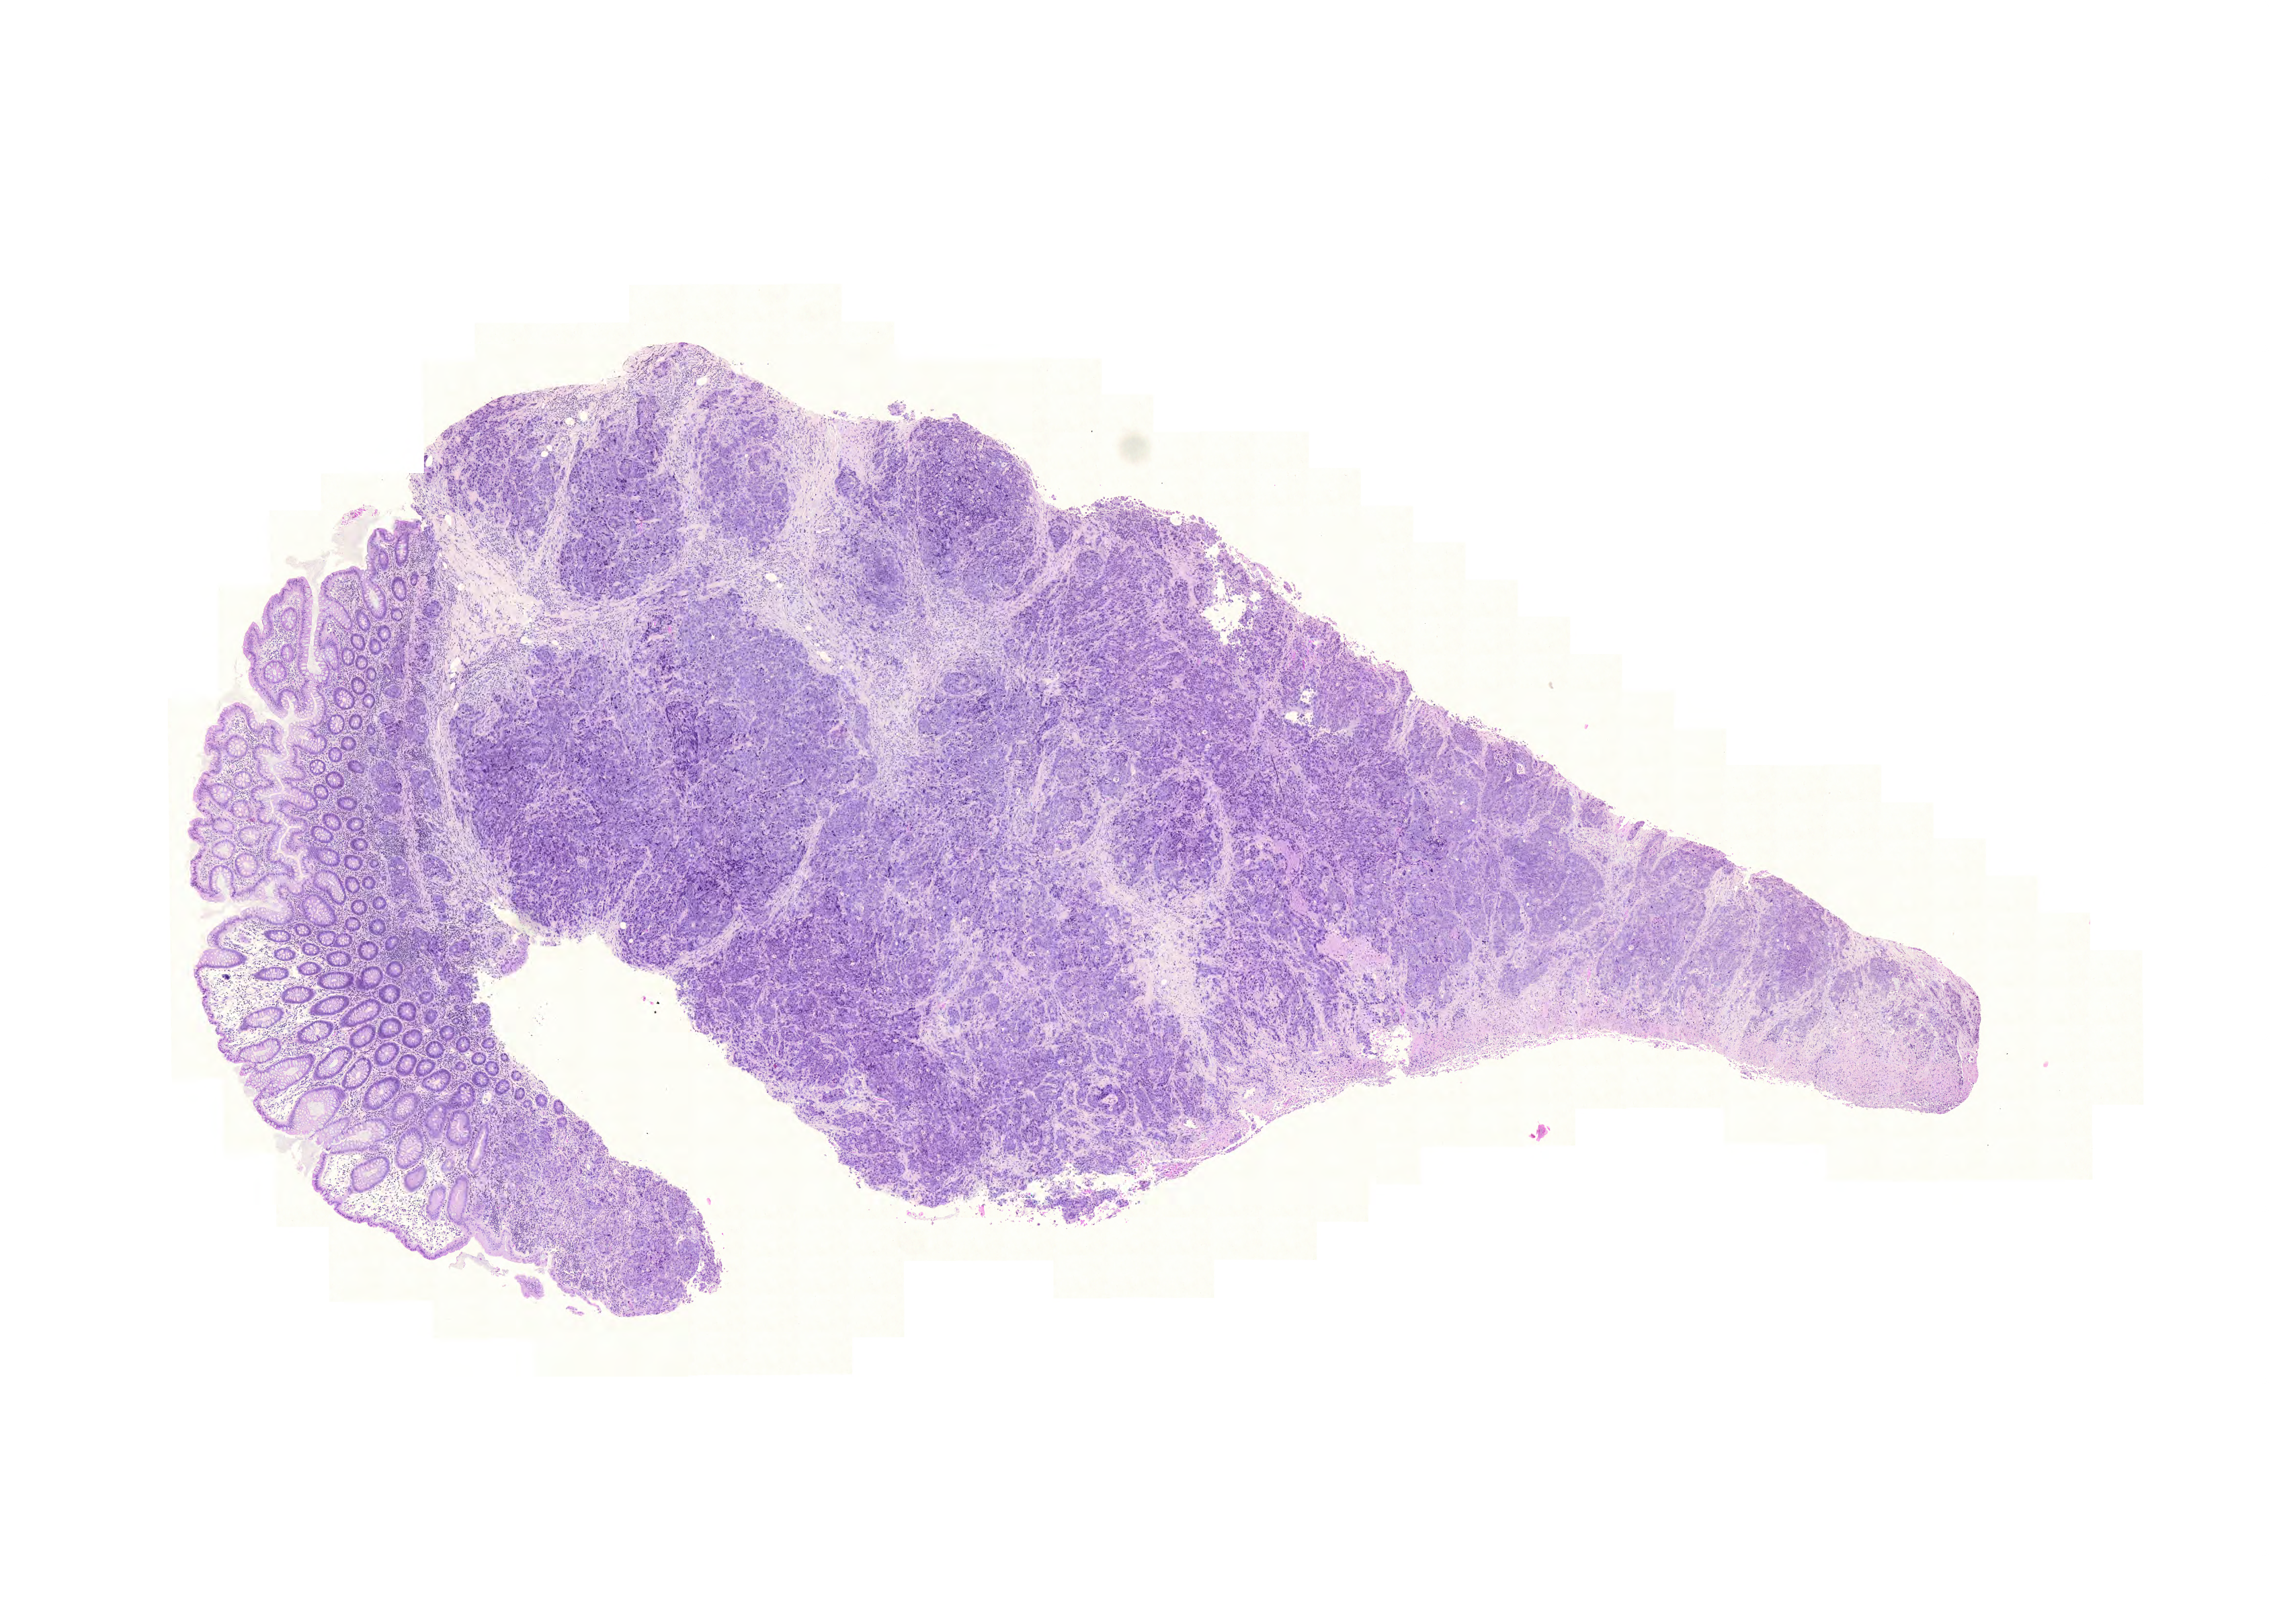
Digitized Hematoxylin and eosin (H&E) stained tissue section (whole slide), shown as a low-resolution overview of the whole scanned area (about 12.6 x 9.0 mm, acquisition: 20x scan), formalin-fixed paraffin-embedded (FFPE) diagnostic section, sample: primary tumour, colon. Male patient; age at initial diagnosis 66 years.
* AJCC pathologic stage: IV (6th edition)
* pathologic diagnosis: Adenocarcinoma, NOS (ascending colon)